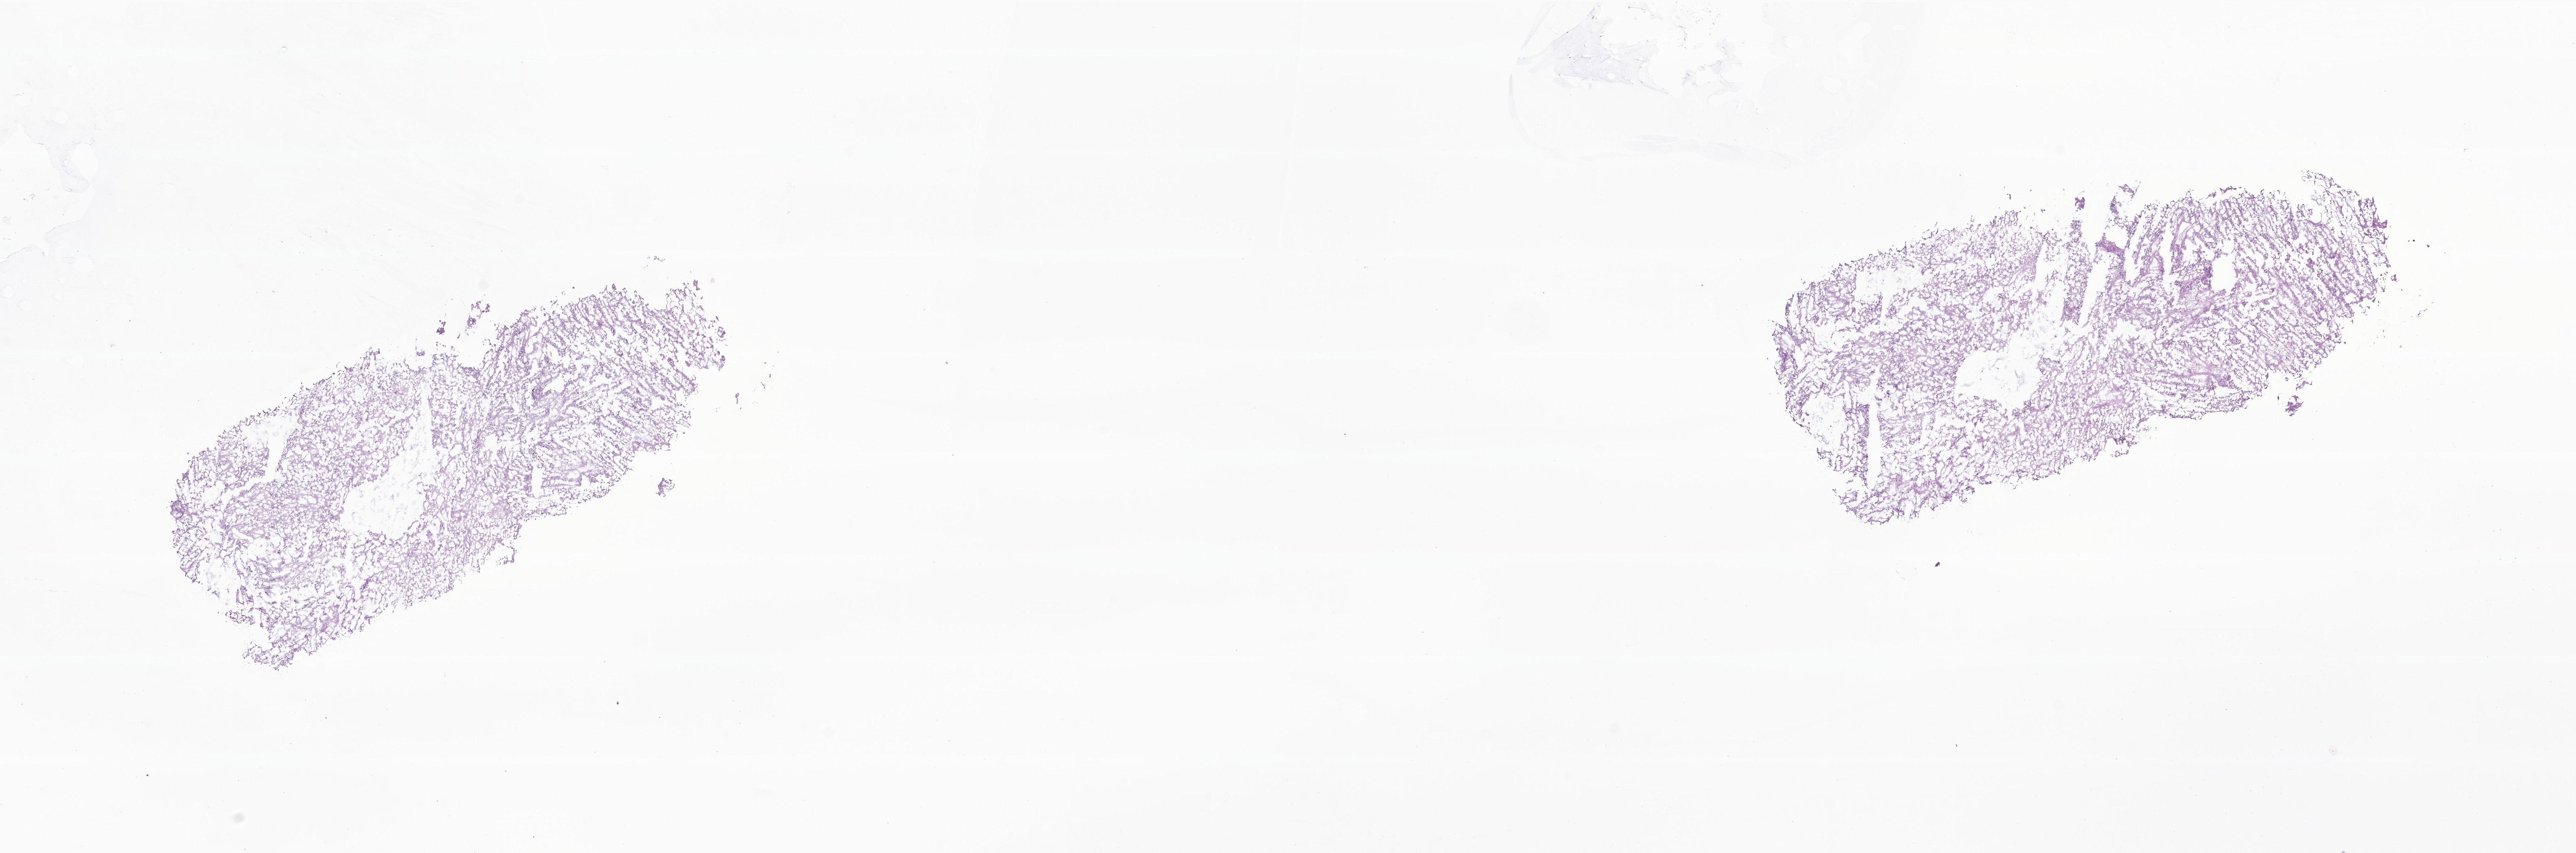
Whole-slide image, haematoxylin and eosin stain of tumor tissue from the cerebral ventricle — a low-resolution overview of the entire scanned area, about 27.2 x 9.0 mm. Frozen section (OCT-embedded). Patient female; age 76 months (6 years 4 months).
* diagnosis: Choroid plexus papilloma, NOS